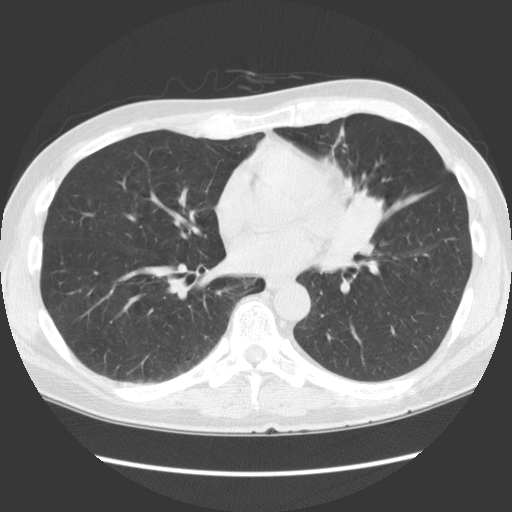
Low-dose screening chest CT, one axial slice; position 62 of 136 along the scan axis; reconstruction kernel STANDARD; lung window (W 1500 / L -600 HU); 2.5 mm slice thickness; 512 × 512 image matrix, field of view 360 × 360 mm.
Outlined on this slice (manually delineated by an expert):
- lesion 1 (tumor, hilum of left lung): box from (x=346, y=188) to (x=385, y=240) px